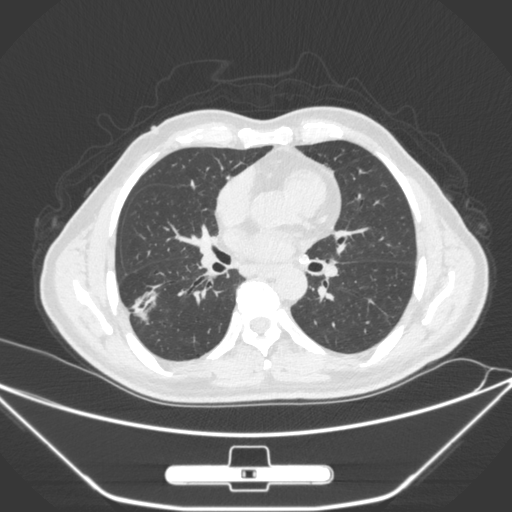
Chest CT, one axial slice; position 146 of 310 along the scan axis; 120 kVp; lung window (W 1500 / L -600 HU); 512 × 512 image matrix, field of view 398 × 398 mm. Patient: male, 71 years. Case-level facts recorded for this patient, not image findings: clinical TNM (as recorded): T1c N0 M0.
Annotated regions visible in this slice (rectangle marked by the reading radiologist):
- lung tumour (recorded histology: adenocarcinoma): bounding box (x1, y1, x2, y2) in pixels: (130, 286, 157, 328)